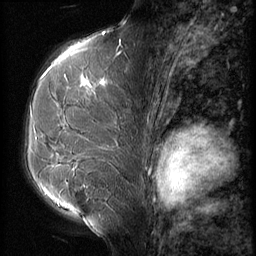
Breast MRI (dynamic contrast-enhanced), one sagittal slice. Slice 37 of 56 in the series (ordered by position). 3 images stored at this slice position (order not interpretable as contrast timing). 1.5 T. TE 4.2 ms, TR 9 ms. 256 × 256 image matrix, field of view 180 × 180 mm. Female patient, age 51 years. From the clinical record (not read from this slice): setting: breast cancer imaged before/during neoadjuvant chemotherapy; receptor status: HR-positive, HER2-negative.
Outlined on this slice (semi-automatically segmented with operator editing):
- analysis volume of interest (the breast-tissue region the enhancement analysis was run in; not a lesion): box from (x=23, y=56) to (x=143, y=165) px
- tumour enhancement mask (voxels above the 140 % enhancement threshold inside the analysis volume of interest): (x=46, y=72)–(x=112, y=149)